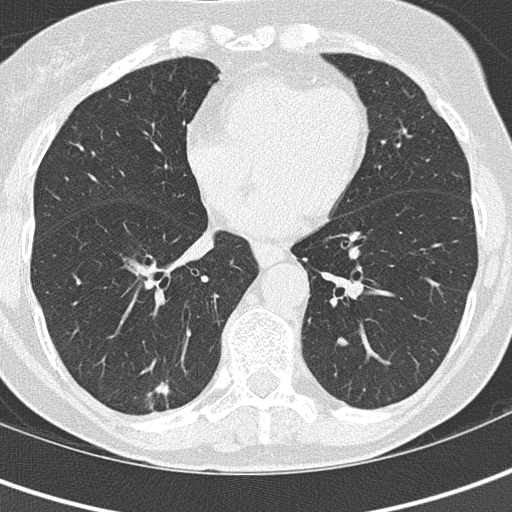
Low-dose screening chest CT, axial slice; second annual screen; lung window (W 1500 / L -600 HU); slice 94 of 152 in the series; 512 × 512 image matrix, field of view 280 × 280 mm. Female, age 69 years at enrolment. Current smoker at enrolment.
- Expert reader's lesion annotation, bounding box (x1, y1, x2, y2) in pixels: (124, 363, 185, 420).
- The screening reader recorded 2 non-calcified nodules or masses ≥4 mm on this exam; which of them this box marks is not recorded.
- Official screen result: positive, other.
- Later outcome: lung cancer diagnosed 112 days after this screen — adenocarcinoma, NOS, right lower lobe, moderately differentiated (G2), stage IA (AJCC 6th edition), 16 mm at pathology.